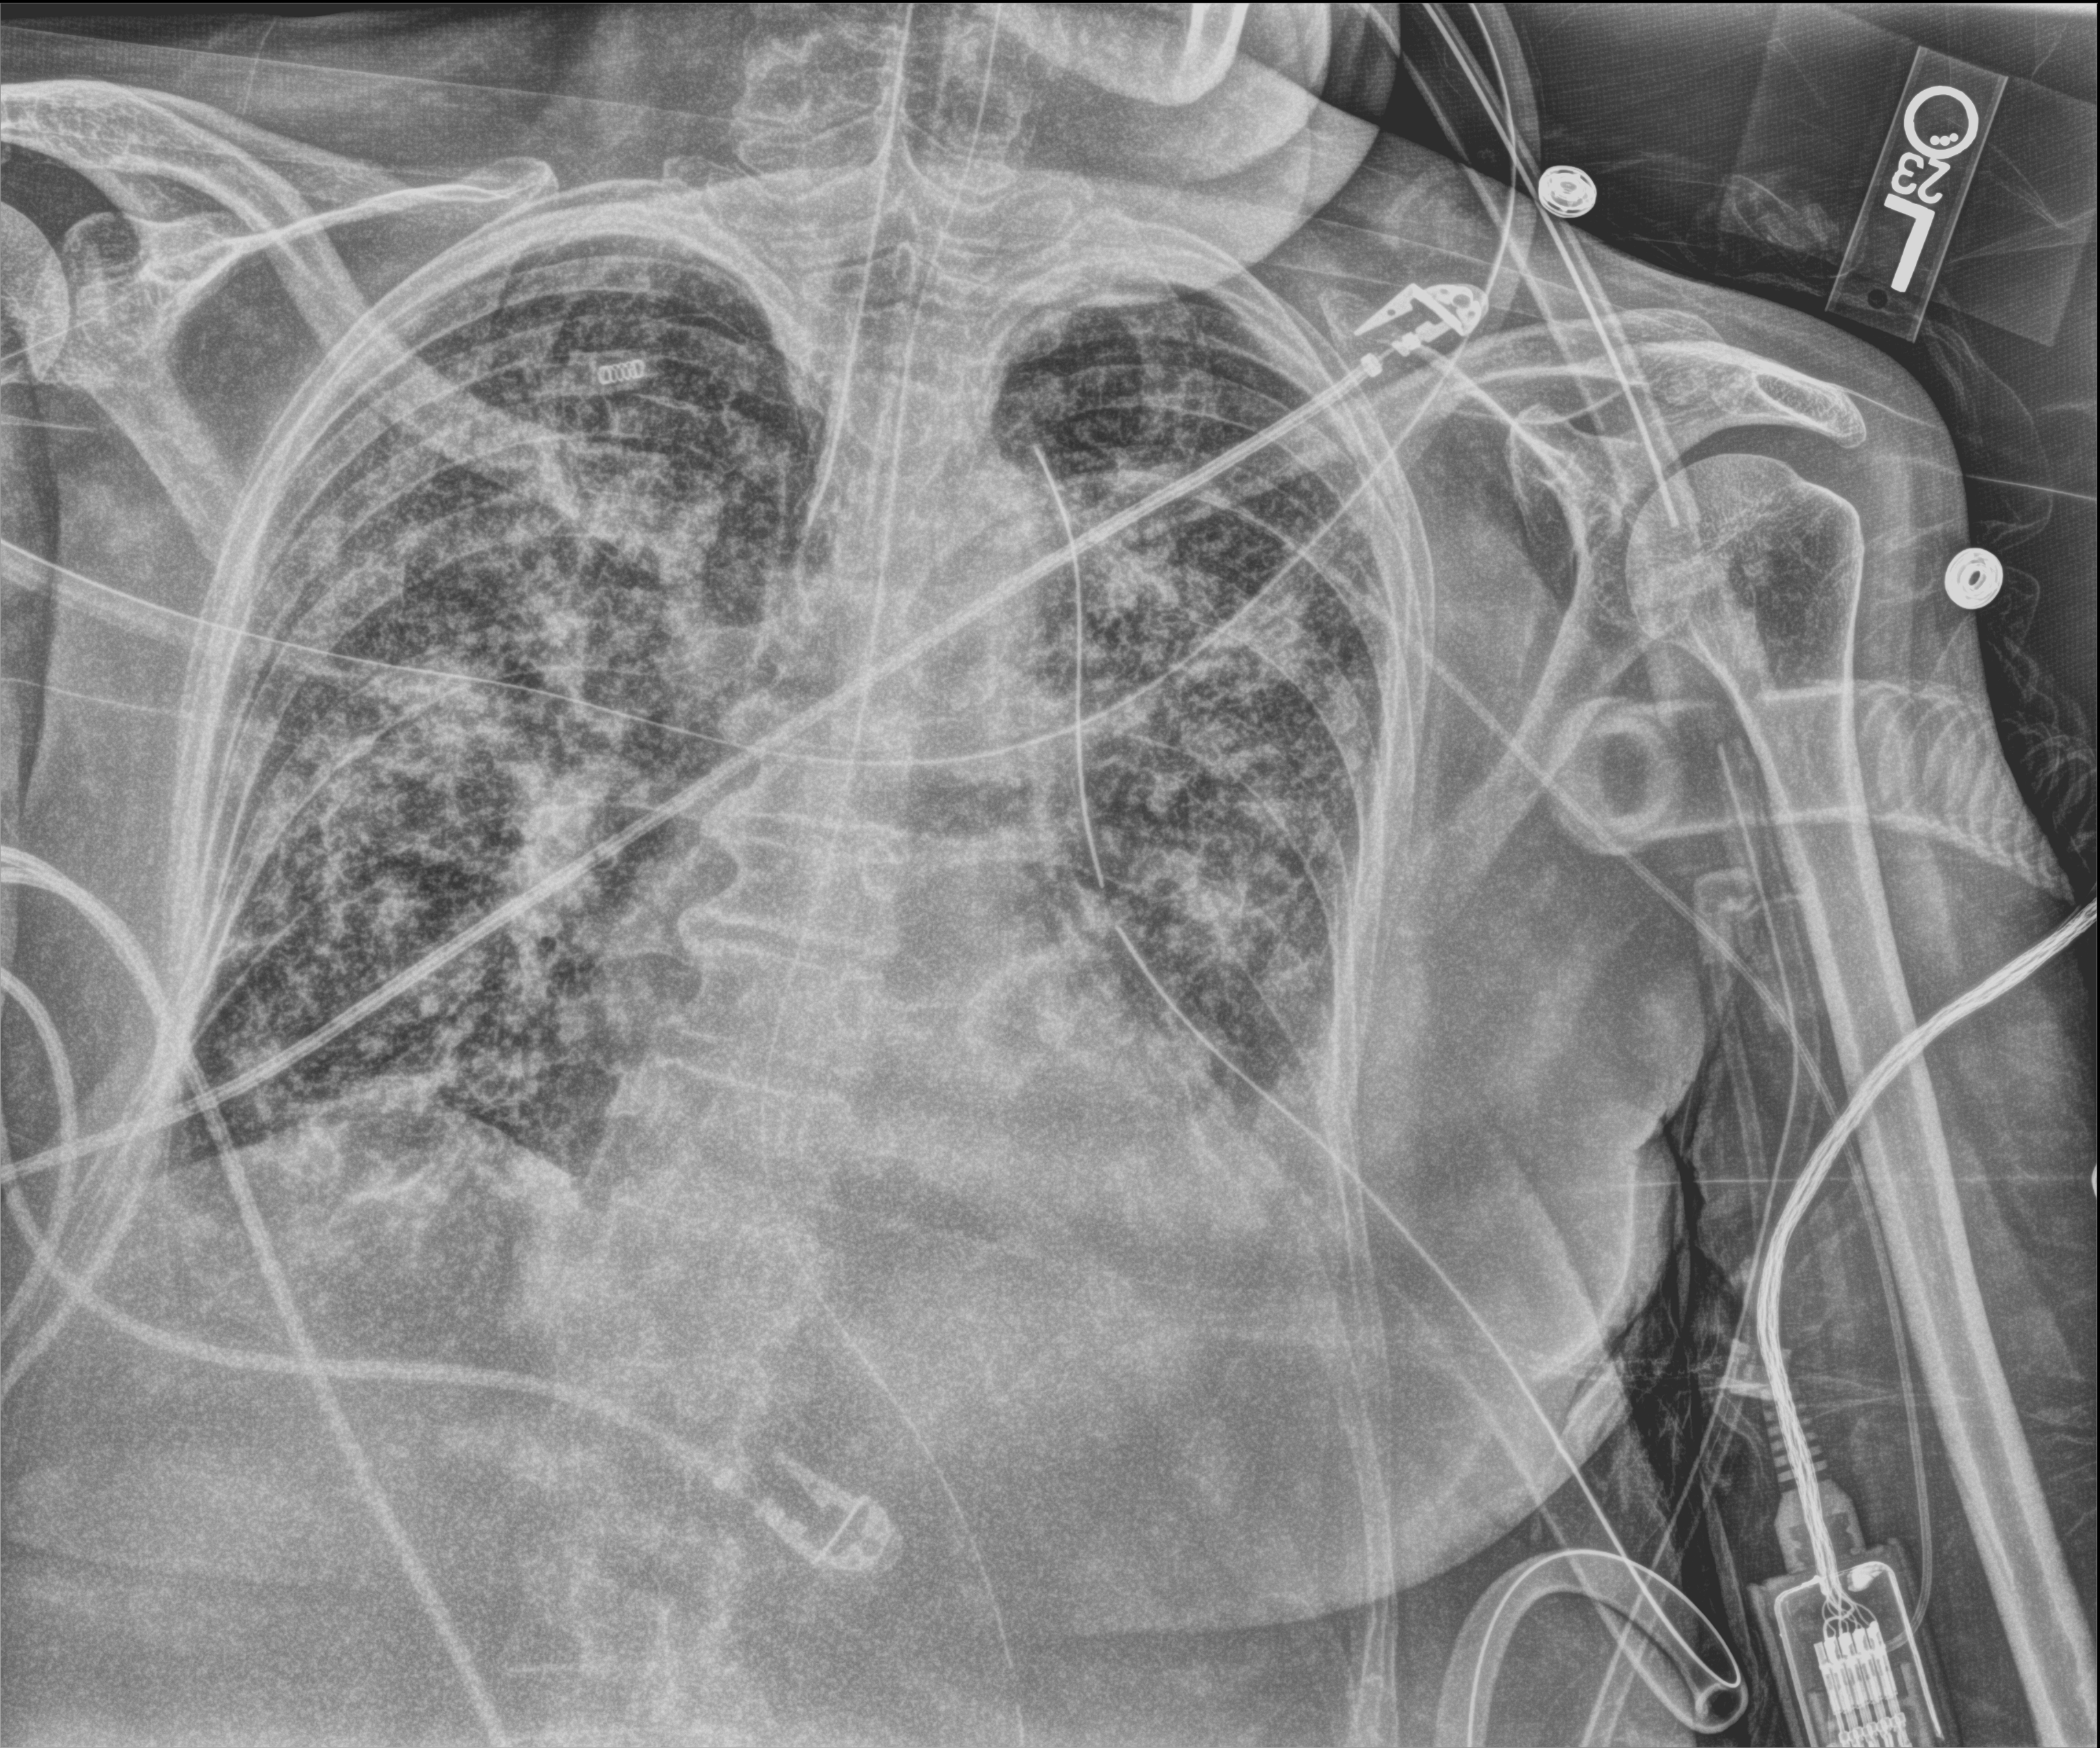
Portable chest radiograph, anteroposterior (AP) projection. Female patient hospitalised with COVID-19, age 75–90 years.
Admission-level facts for this patient (not findings on this image; timing relative to this image not recorded): mechanically ventilated during this hospital stay: yes; smoking status (admission record): former; chronic kidney disease (admission record): no.